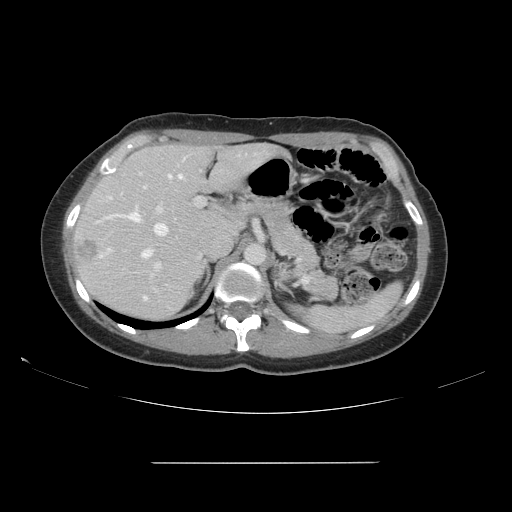
Contrast-enhanced abdominal CT, one axial slice. Position 103 of 151 along the scan axis. 120 kVp. Intravenous contrast given. Soft-tissue window (W 400 / L 40 HU). 512 × 512 image matrix. Female patient, age 46 years. Case-level facts recorded for this patient, not image findings: diagnosis: colorectal cancer liver metastases, imaged before liver resection; multiple liver metastases: yes; largest metastasis: 3 cm; disease in both lobes: yes.
Outlined on this slice (expert manual segmentation):
- hepatic veins: bounding box <97,174,183,259> (left, top, right, bottom; pixels)
- liver: <73,144,278,321>
- planned liver remnant (the part of the liver to remain after resection): <89,145,280,255>
- portal vein (with intrahepatic branches): <139,172,204,300>
- liver metastasis: <77,241,98,261>